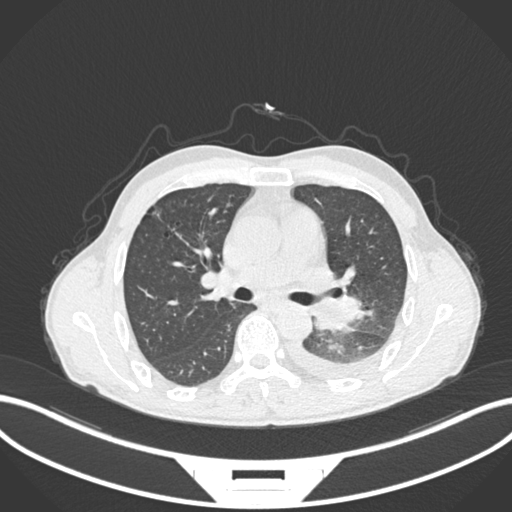
Chest CT, one axial slice. Position 148 of 222 along the scan axis. Reconstruction kernel B30f. 120 kVp. Lung window (W 1500 / L -600 HU). 1 mm slice thickness. 512 × 512 image matrix, field of view 400 × 400 mm. Patient: male, 47 years. Case-level facts recorded for this patient, not image findings: clinical TNM (as recorded): T3 N1 M1c; histopathological grade: G3.
Structures marked on this image (rectangle marked by the reading radiologist):
- lung tumour (recorded histology: small cell carcinoma): box from (x=304, y=294) to (x=367, y=336) px